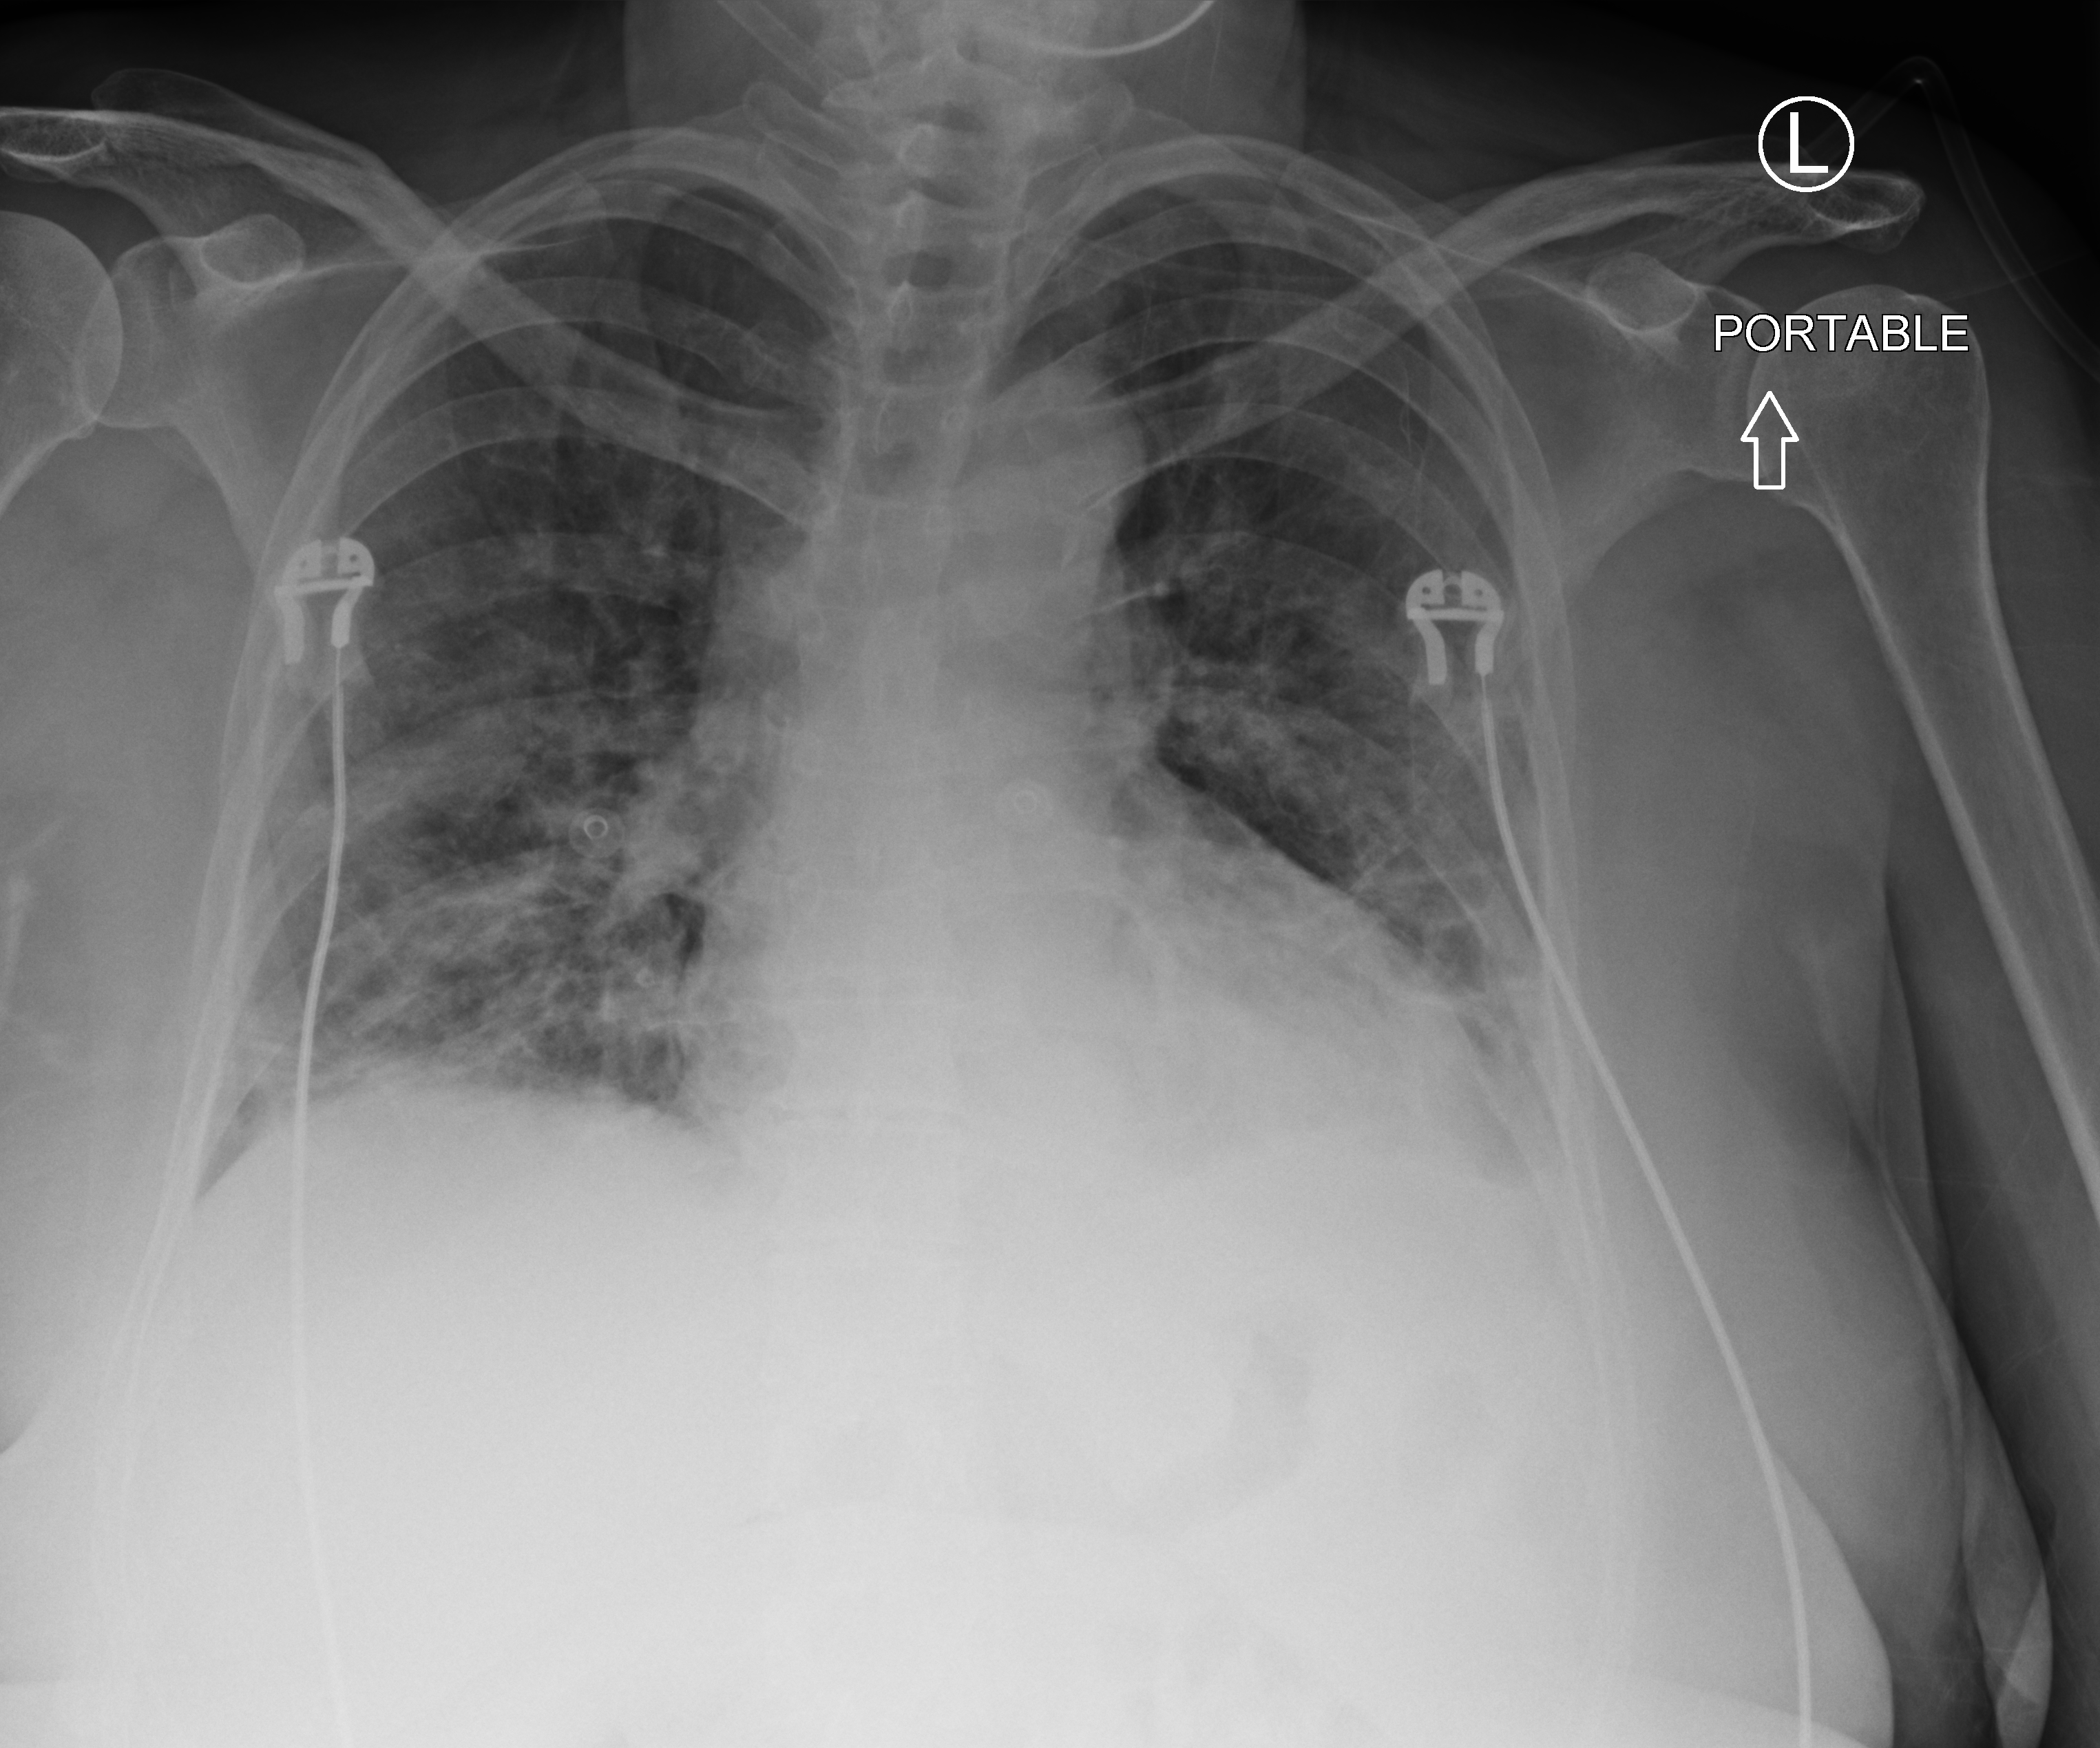
Bedside chest radiograph (computed radiography); anteroposterior (AP) projection. Female patient hospitalised with COVID-19, age 60–74 years.
Hospital-stay facts (about this admission, not read from this image; timing relative to this image not recorded):
- admitted to intensive care during this hospital stay: no
- mechanically ventilated during this hospital stay: no